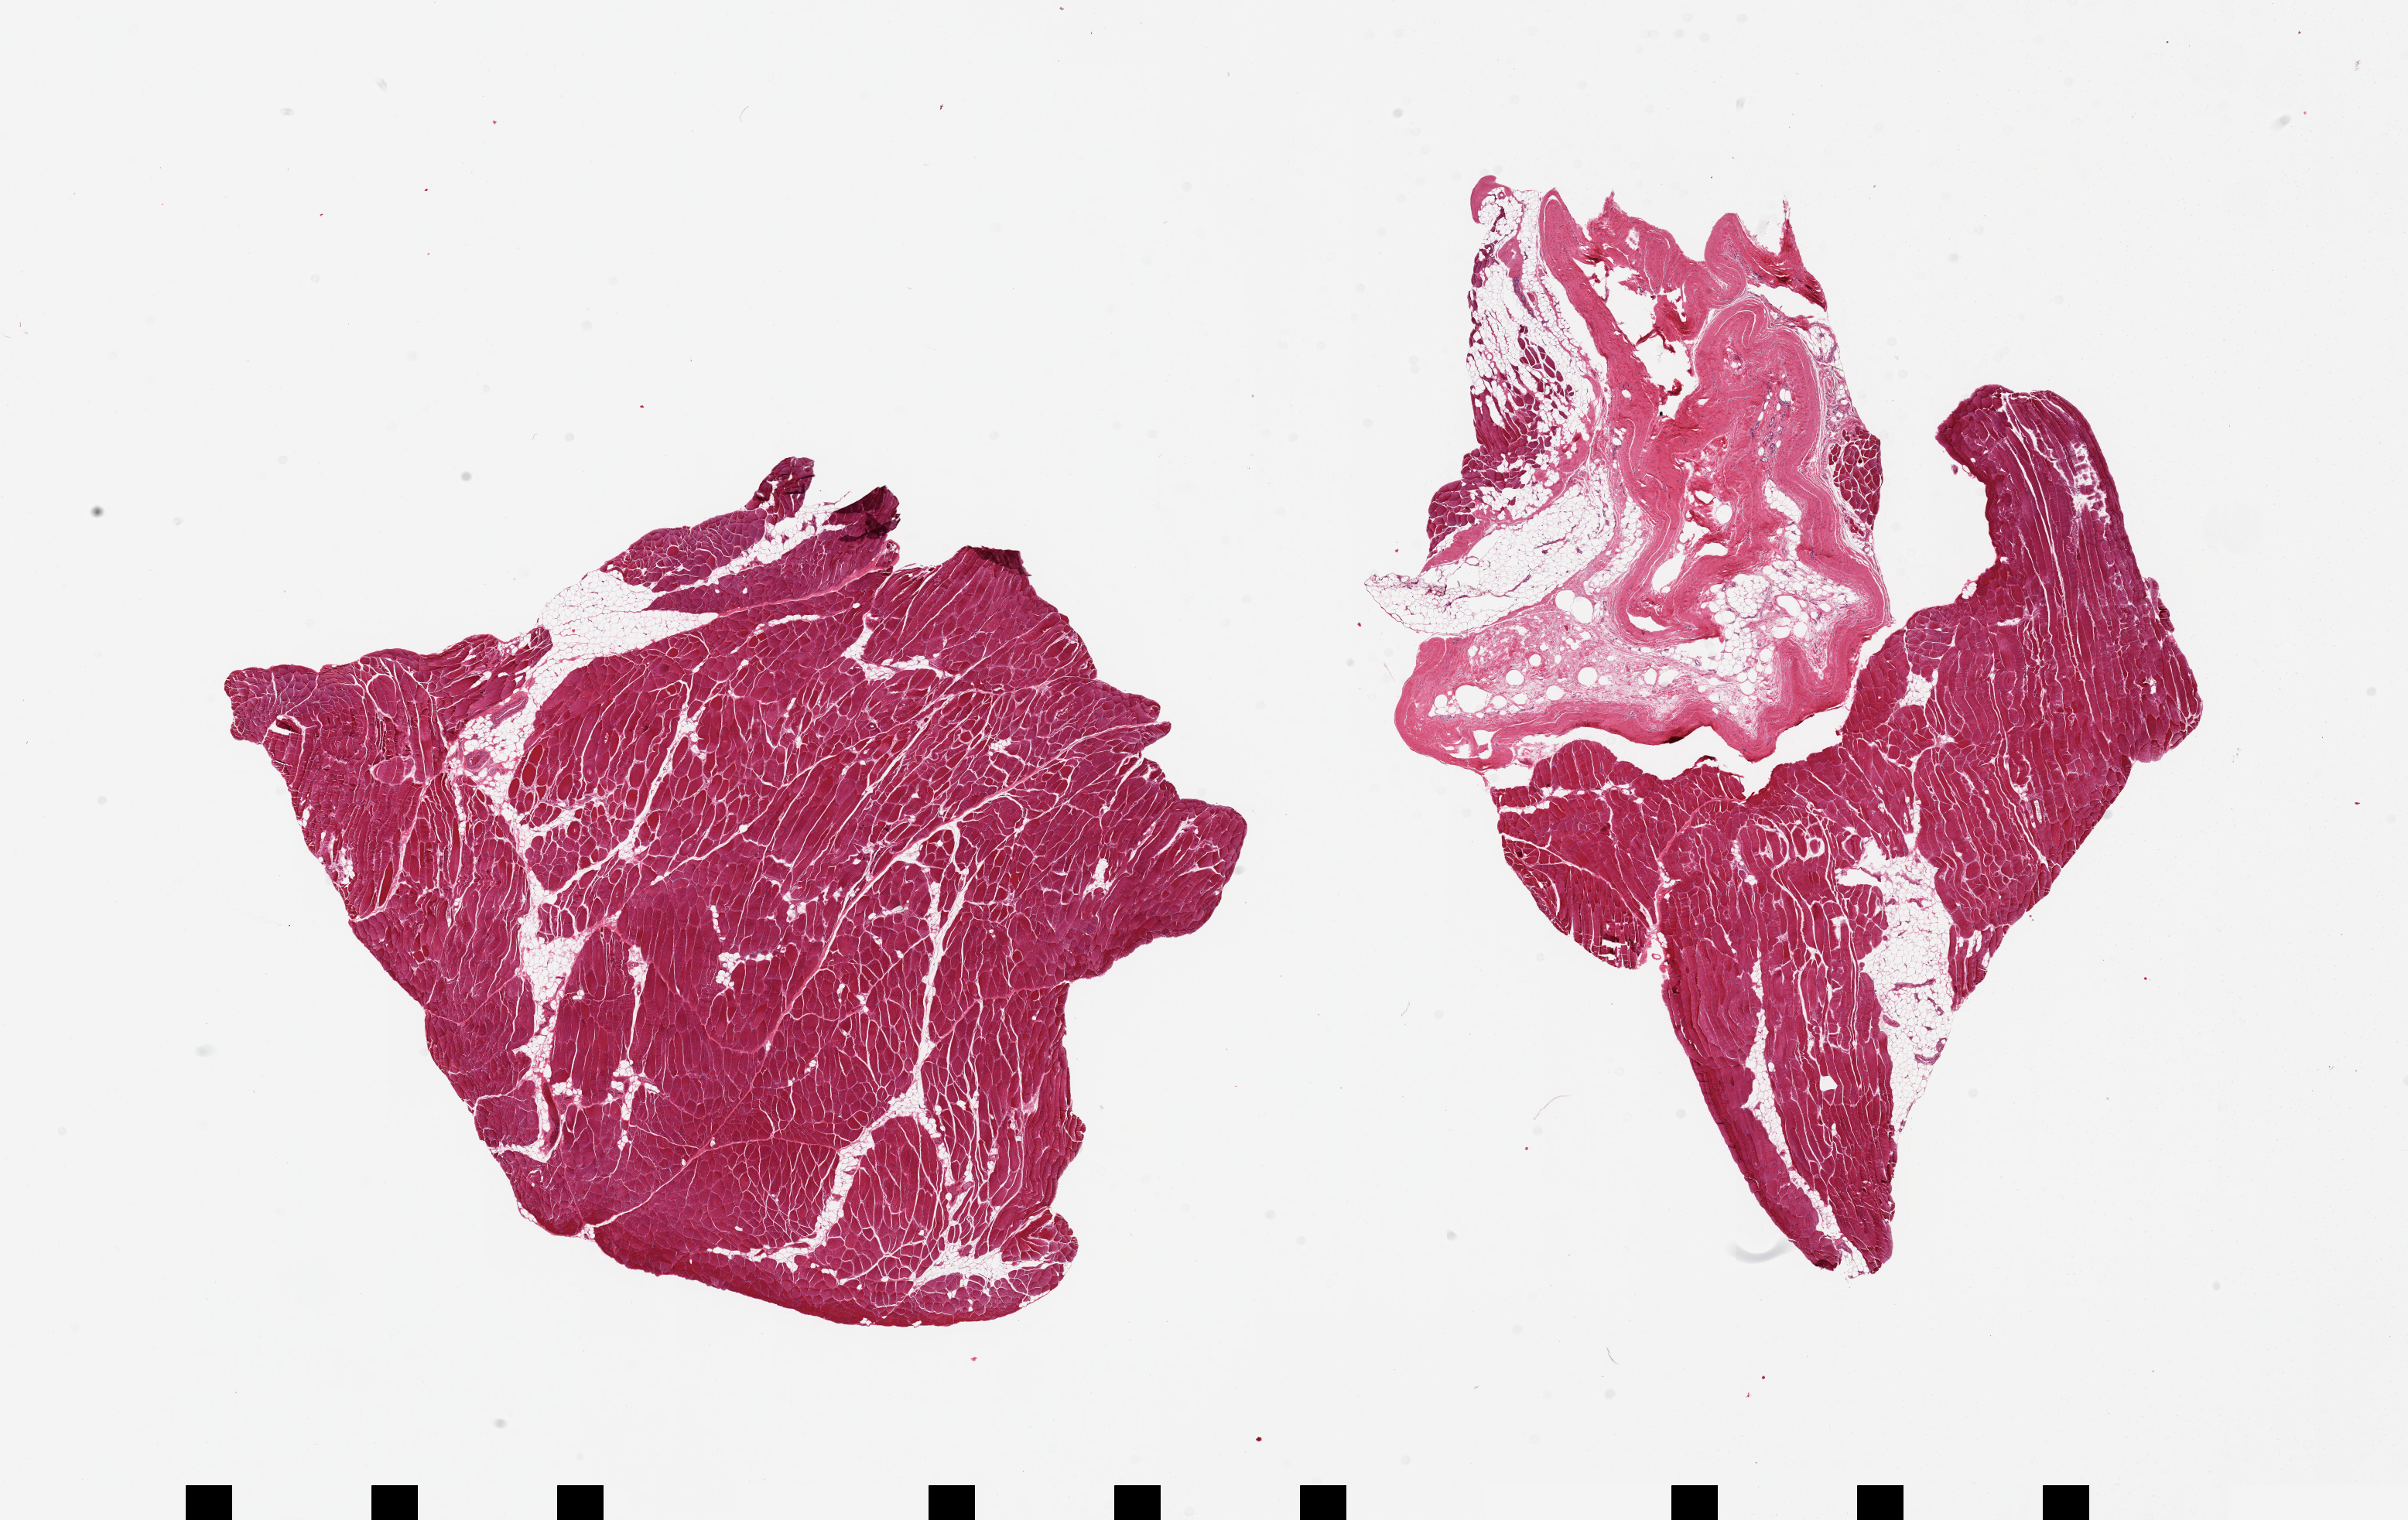
Whole-slide image, H&E stain — whole scanned area (about 24.6 x 15.5 mm, slide scanned at 20x) shown as a low-resolution overview; PAXgene-fixed, paraffin-embedded tissue; section of skeletal muscle (target tissue); donor tissue sample. Donor sex: male.
Reviewer comment on this tissue sample: 2 pieces, 10.5x8 and 9x7mm; one with ~5% interstitial fat; the other is 50% adherent fibroadipose tissue.